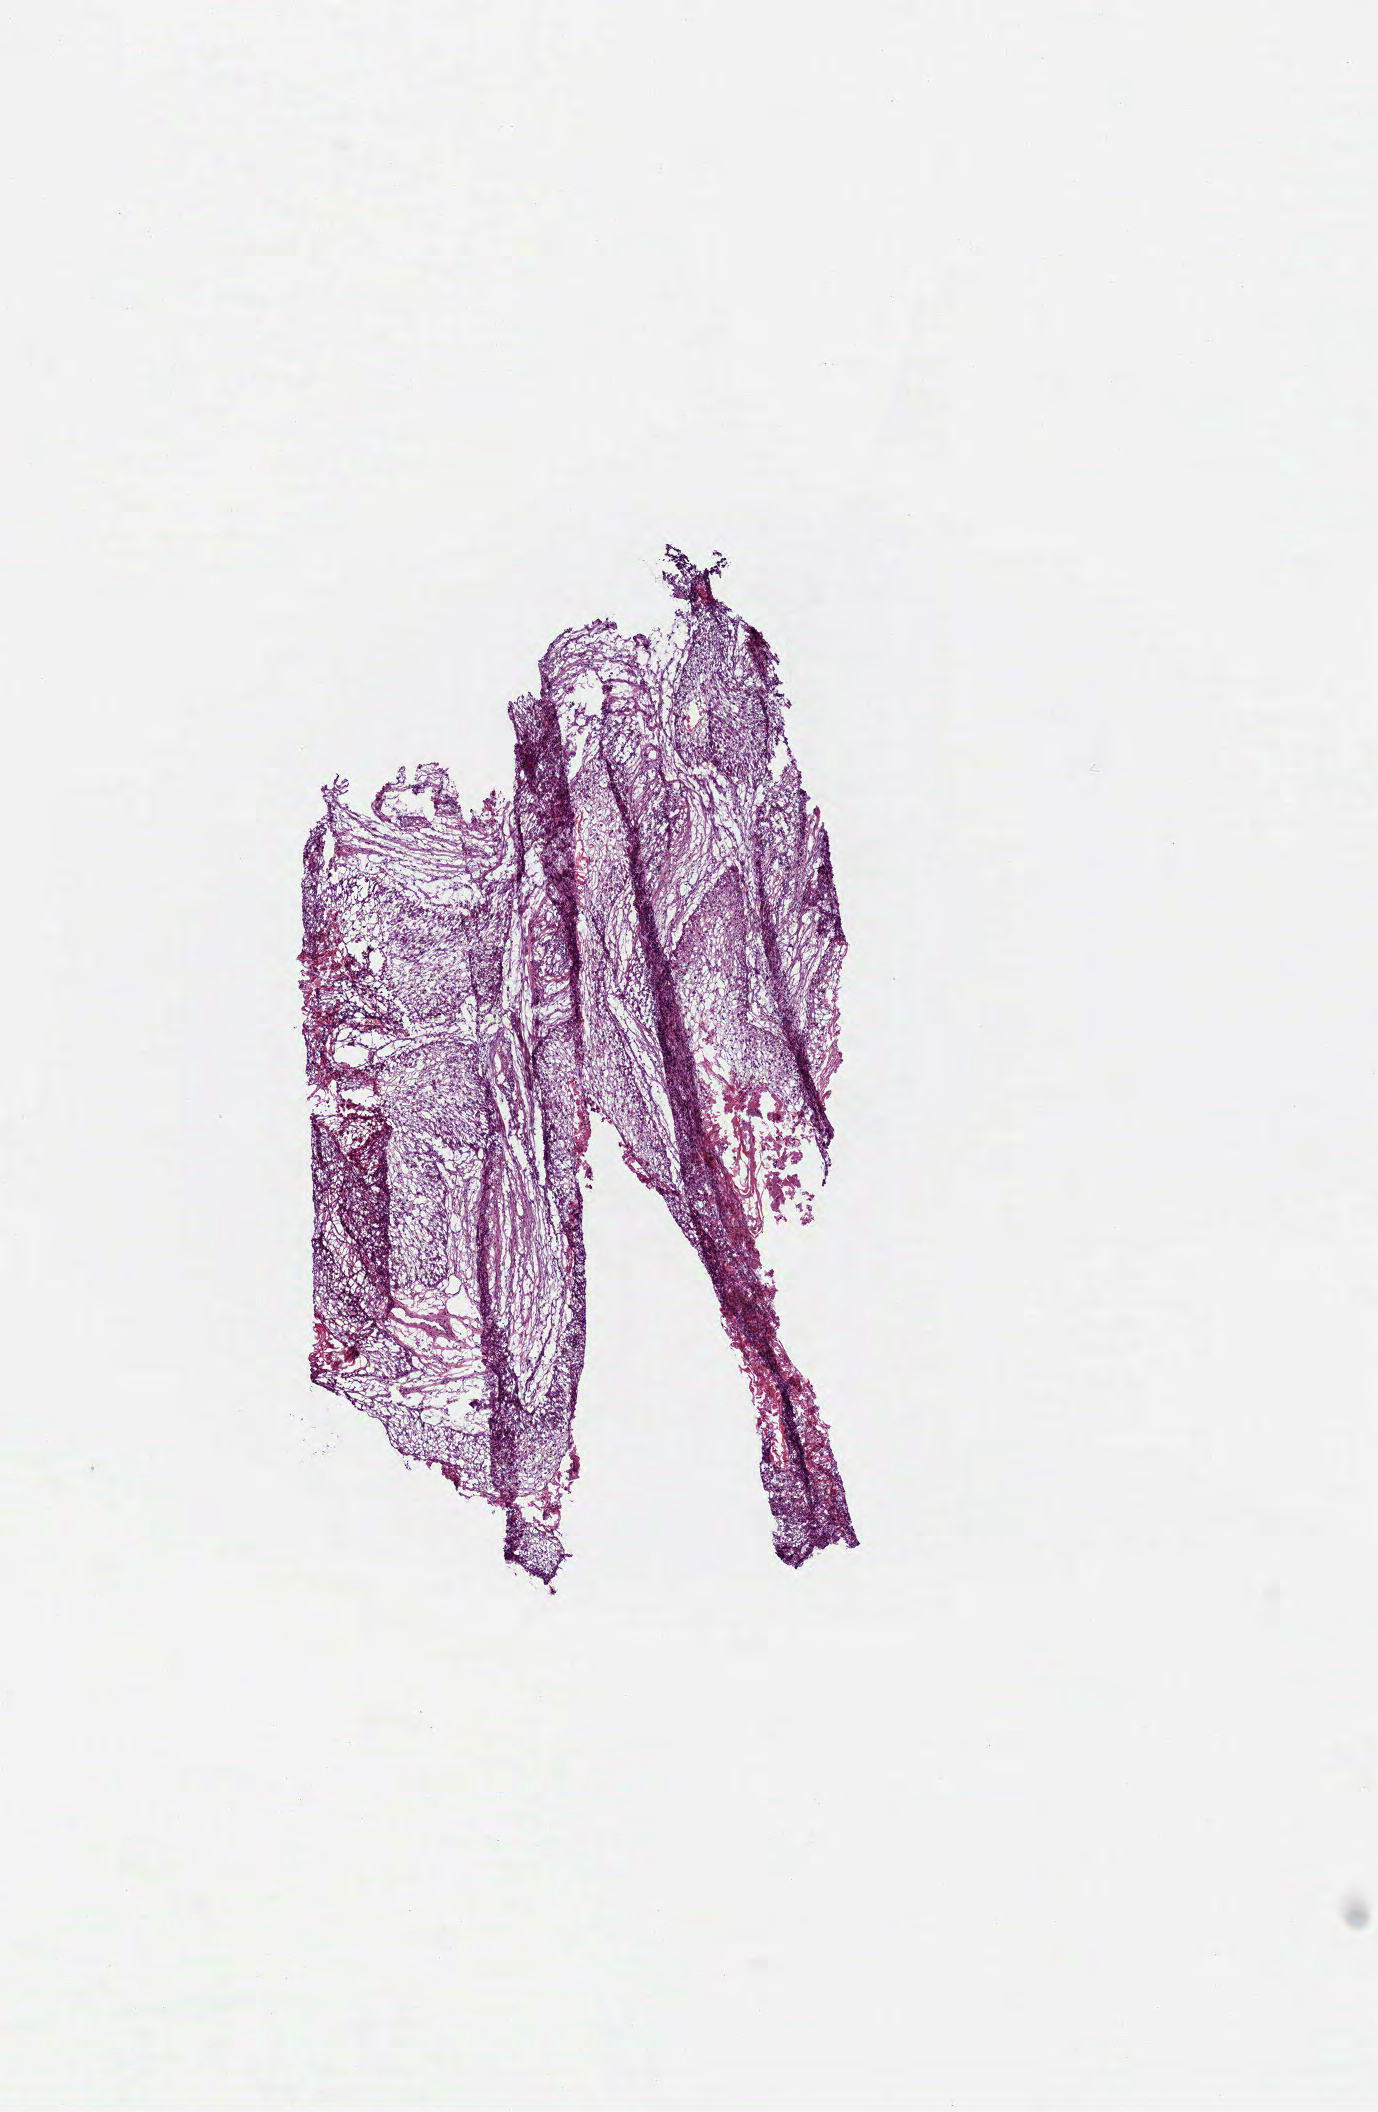
H&E whole-slide image, a low-resolution overview of the entire scanned area, about 5.6 x 8.5 mm (slide scanned at 40x). Frozen section from the top of the tissue portion. Primary tumour sample from the head and neck. Patient: male, age at initial diagnosis 51 years. Histologic grade: G2 (moderately differentiated). Slide review estimates, as recorded: tumour cells 90%, tumour nuclei 80%, normal cells 0%, stromal cells 0%, necrosis 10%.
- lymph nodes positive (case pathology): 0 of 29 examined
- AJCC pathologic stage: III (7th edition)
- diagnosis: Squamous cell carcinoma, NOS (tongue, NOS)